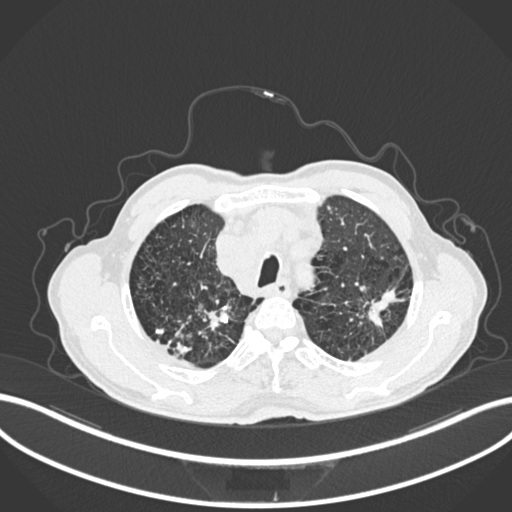
Chest CT, one axial slice; reconstruction kernel B30f; 120 kVp; lung window (W 1500 / L -600 HU); 1 mm slice thickness; 512 × 512 image matrix, field of view 400 × 400 mm. Male patient, age 74 years. From the clinical record (not read from this slice): clinical TNM (as recorded): T2a N1 M0.
Structures marked on this image (rectangle marked by the reading radiologist):
- lung tumour (recorded histology: adenocarcinoma): bounding box [x1, y1, x2, y2] px = [362, 280, 401, 335]